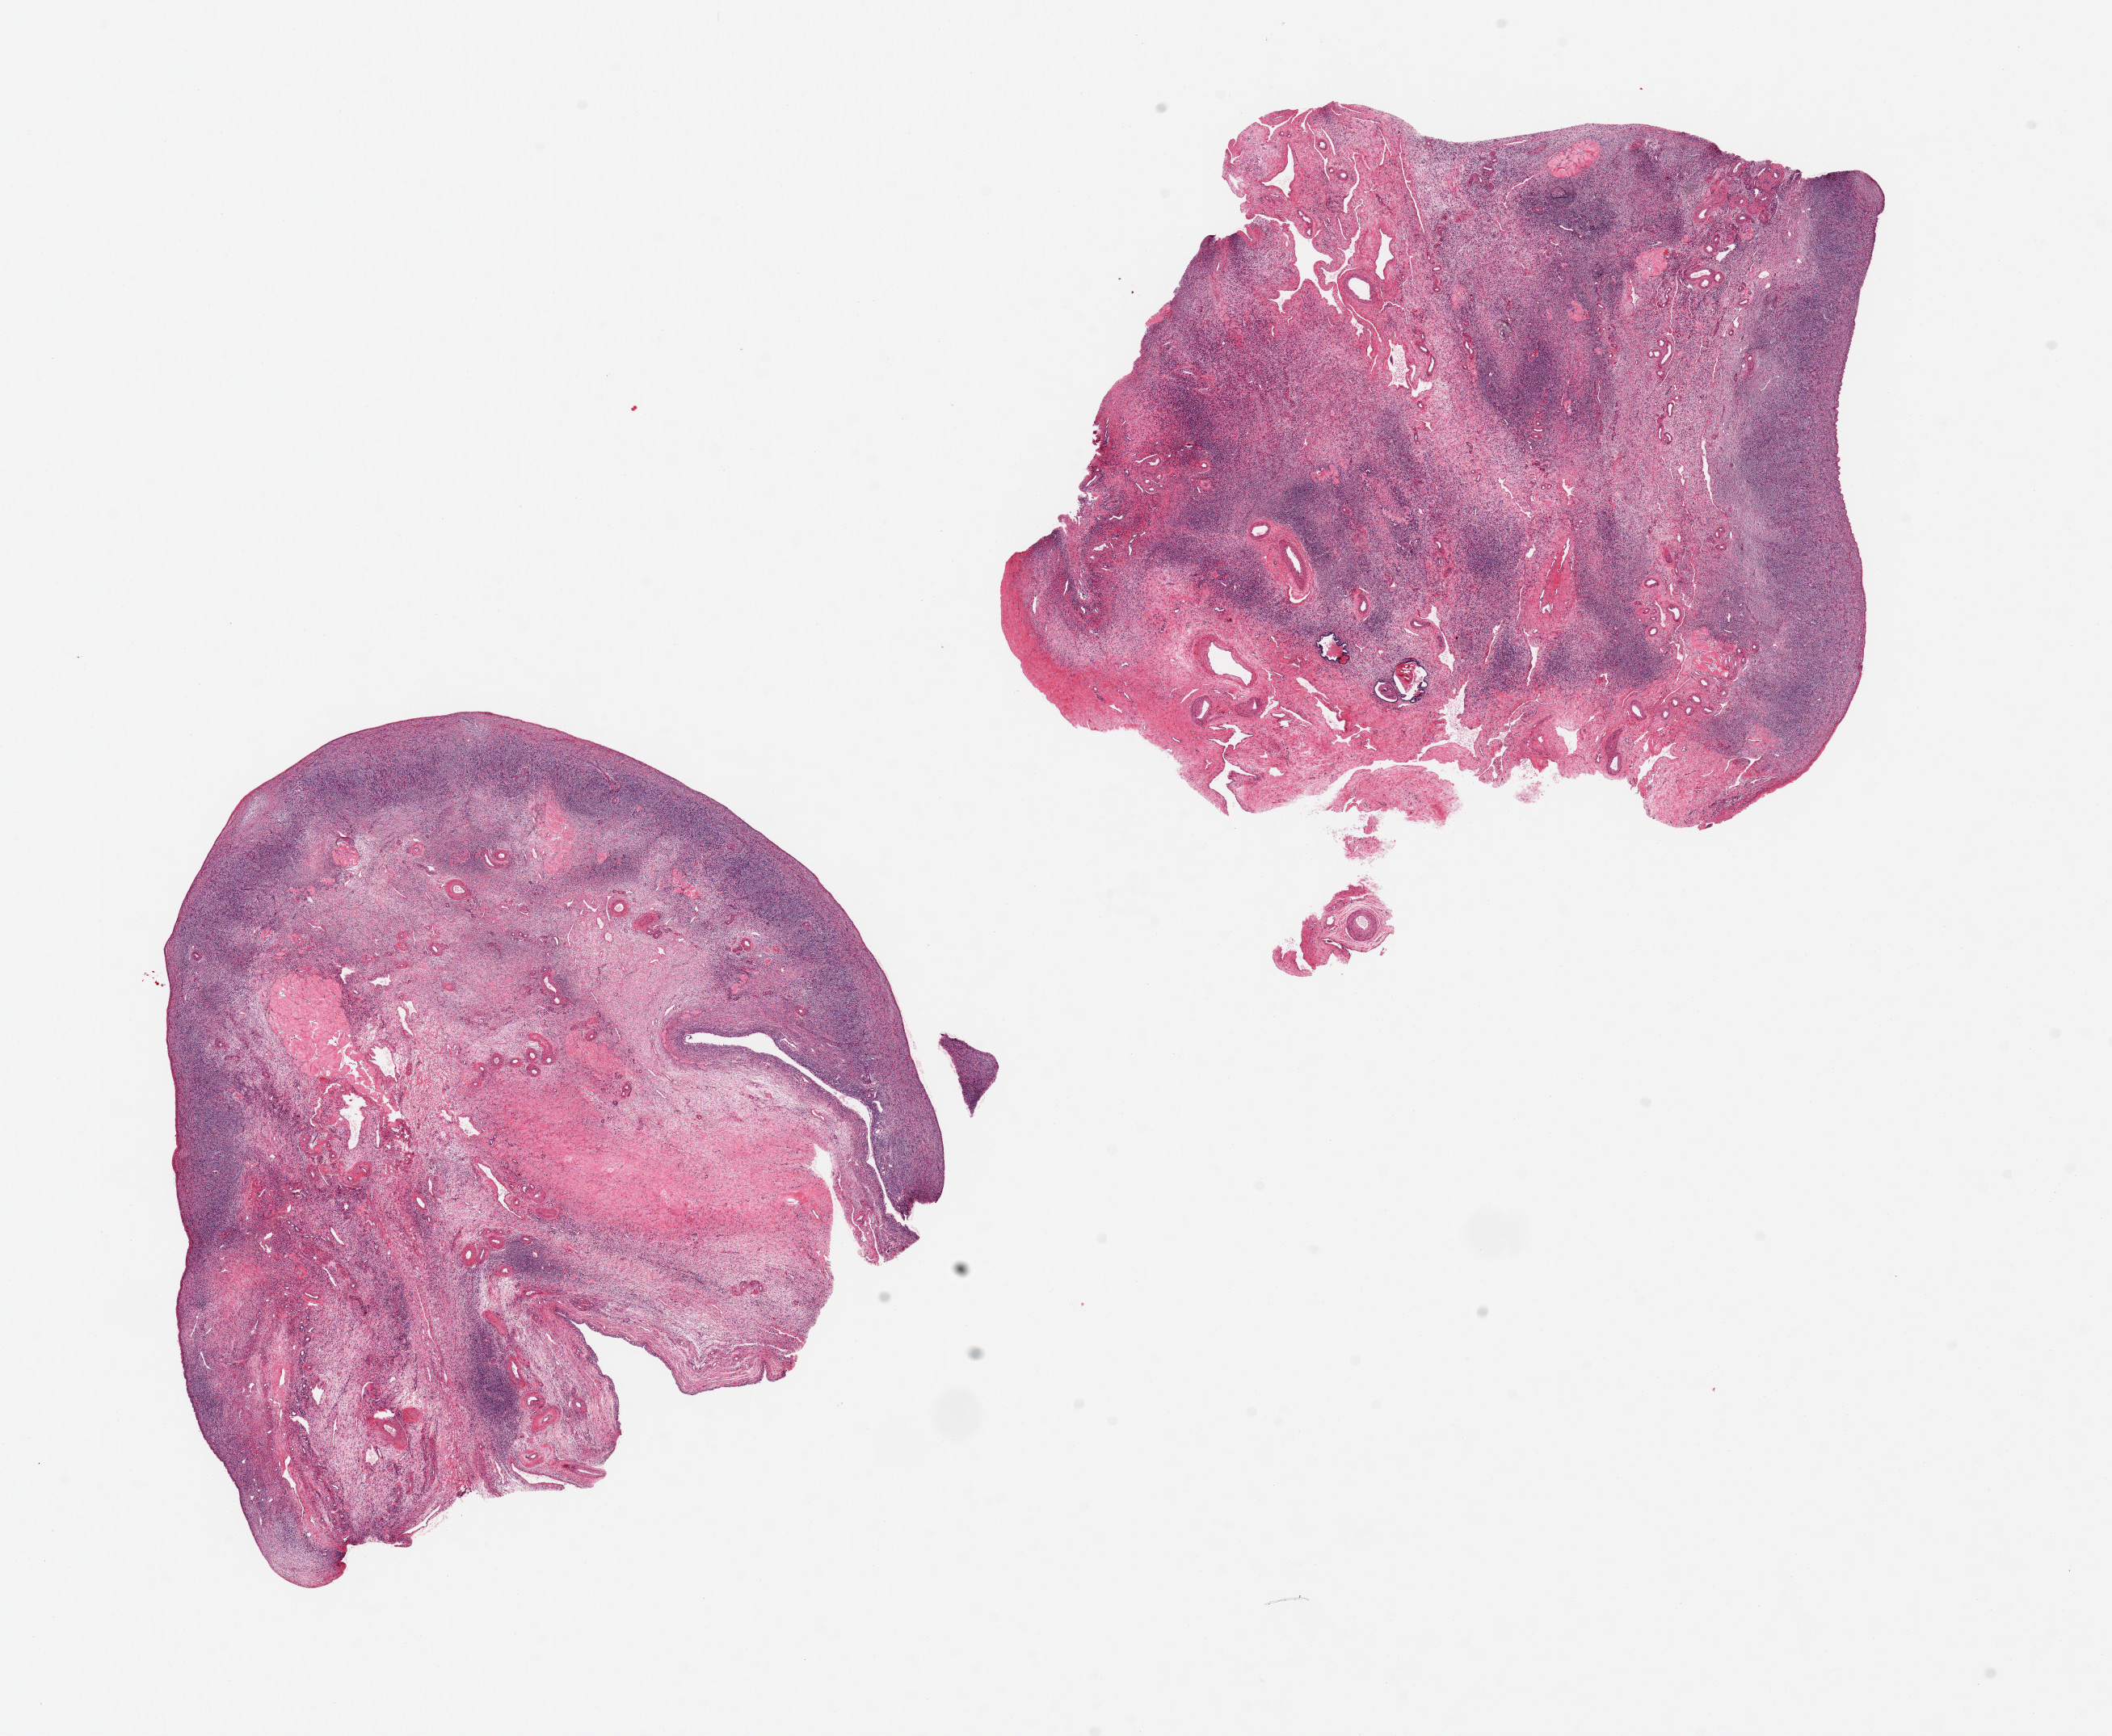
H&E whole-slide image — shown as a low-resolution overview of the whole scanned area (about 20.7 x 17.0 mm, slide scanned at 20x). PAXgene-fixed, paraffin-embedded tissue. Sampled site (target tissue): ovary. Tissue donor sample. Donor sex: female.
Reviewer comment on this tissue sample: 2 pieces ~8x7mm, typical post menopausal atrophy of cortex.